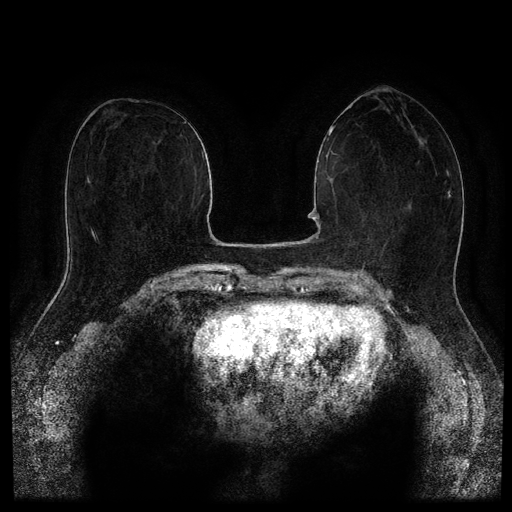
Breast MRI (dynamic contrast-enhanced, multi-phase), one axial slice. Slice 53 of 116 in the series (ordered by position). Dynamic contrast-enhanced series, time point 2 of 5 at this slice position (early post-contrast). 1.5 T. TE 2.6 ms, TR 5.3 ms. 2.1 mm slice thickness. 512 × 512 image matrix, field of view 350 × 350 mm. Patient: female, 66 years.
Outlined on this slice (semi-automatically segmented with operator editing):
- breast lesion (labelled benign in the annotation): bounding box [x1, y1, x2, y2] px = [408, 205, 411, 209]